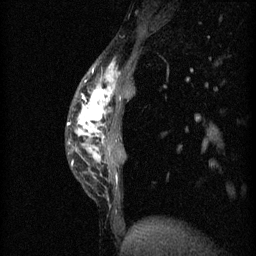
Breast MRI (dynamic contrast-enhanced), one sagittal slice. Position 13 of 60 along the scan axis. 3 images stored at this slice position (order not interpretable as contrast timing). 1.5 T. TE 4.2 ms, TR 11 ms. 2 mm slice thickness. 256 × 256 image matrix, field of view 180 × 180 mm. Patient: female, 40 years.
Structures marked on this image (semi-automatic segmentation, software-assisted and operator-edited):
- analysis volume of interest (the breast-tissue region the enhancement analysis was run in; not a lesion): bounding box (x1, y1, x2, y2) in pixels: (68, 62, 136, 187)
- tumour enhancement mask (voxels above the 70 % enhancement threshold inside the analysis volume of interest): (68, 66, 118, 167)